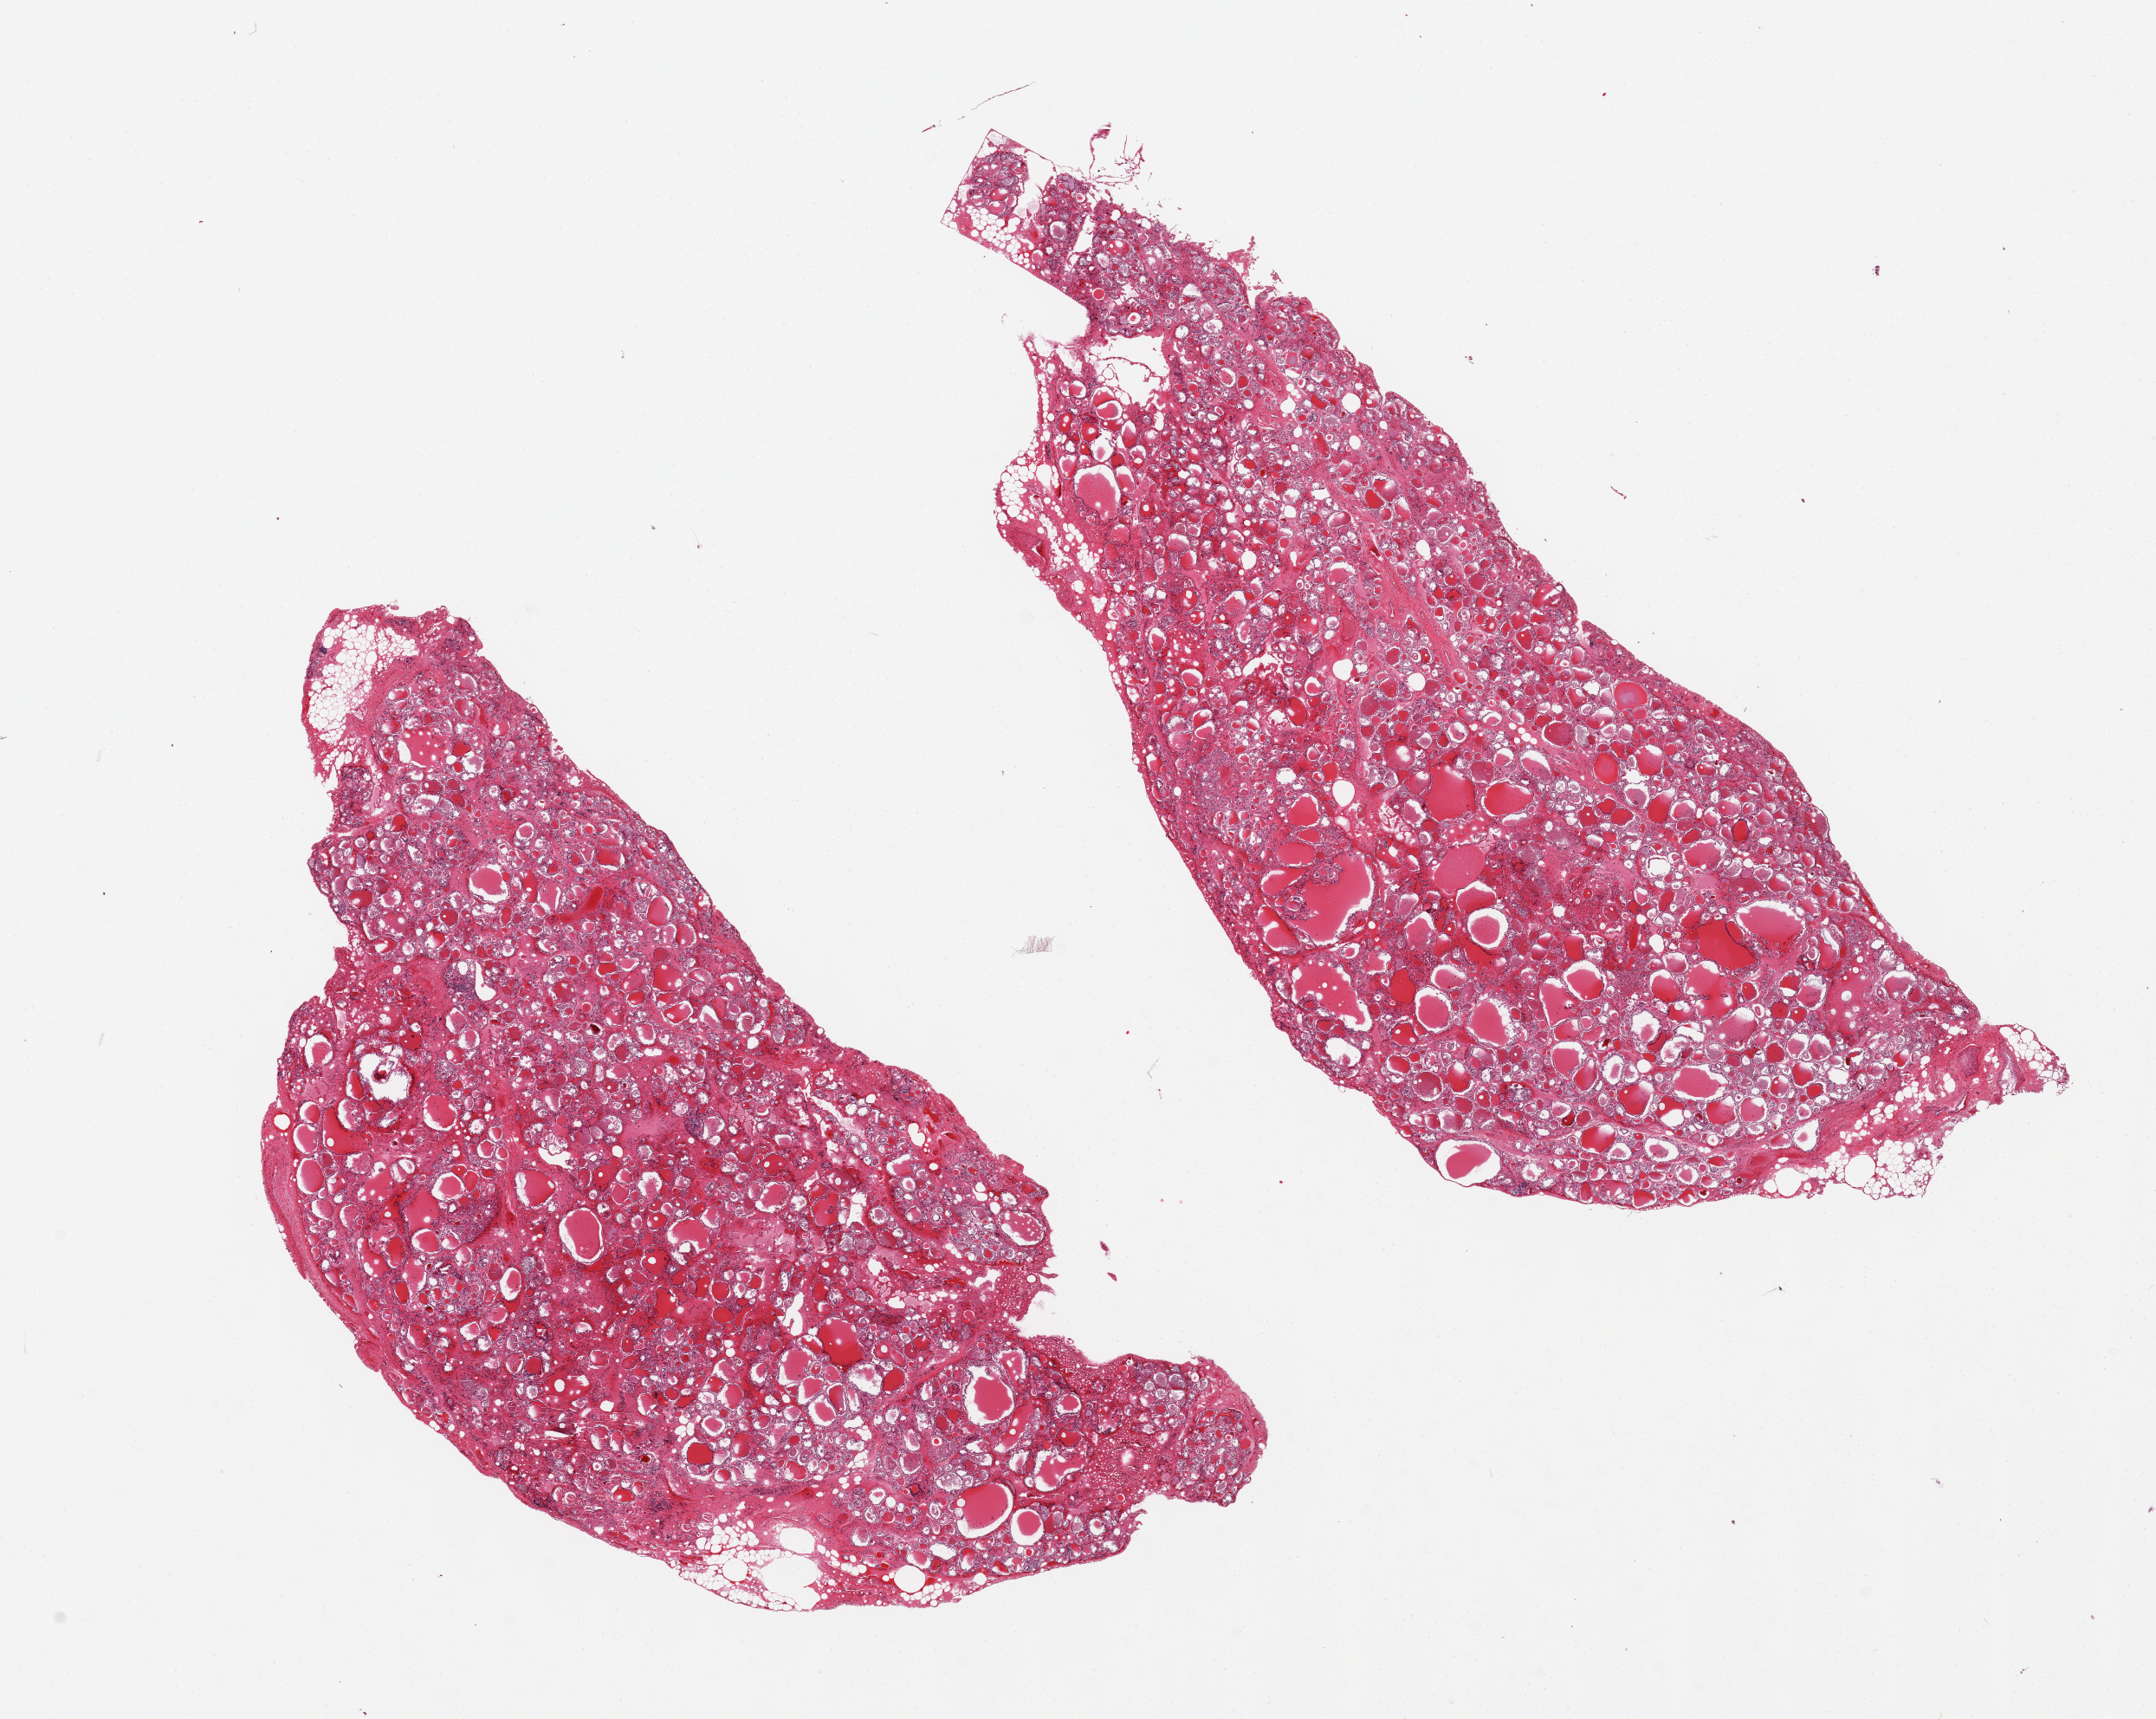
H&E whole-slide image, brightfield — a low-resolution overview of the entire scanned area, about 19.7 x 15.7 mm (acquisition: 20x scan), PAXgene-fixed, paraffin-embedded tissue, section of thyroid (target tissue), tissue donor sample. Donor sex: female.
- review note (as recorded): 2 pieces, badly autolyzed